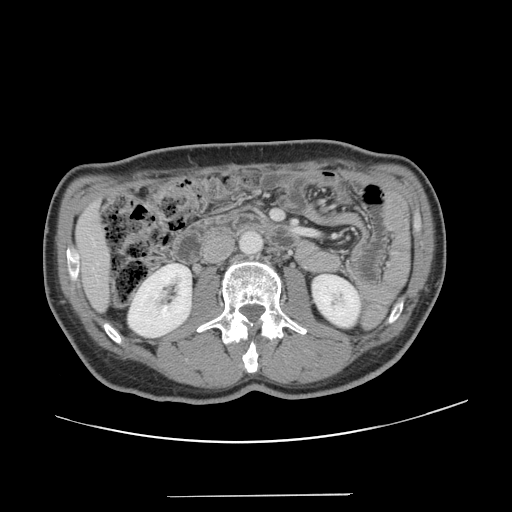
Contrast-enhanced abdominal CT, one axial slice. Position 49 of 131 along the scan axis. Intravenous contrast given. Soft-tissue window (W 400 / L 40 HU). 512 × 512 image matrix, field of view 403 × 403 mm. Male patient, age 60 years. Case-level facts recorded for this patient, not image findings: diagnosis: colorectal cancer liver metastases, imaged before liver resection; multiple liver metastases: no; largest metastasis: 2.5 cm; disease in both lobes: no.
Structures marked on this image (manually delineated by an expert):
- liver: bounding box [x1, y1, x2, y2] px = [78, 207, 109, 309]
- planned liver remnant (the part of the liver to remain after resection): [78, 206, 109, 309]